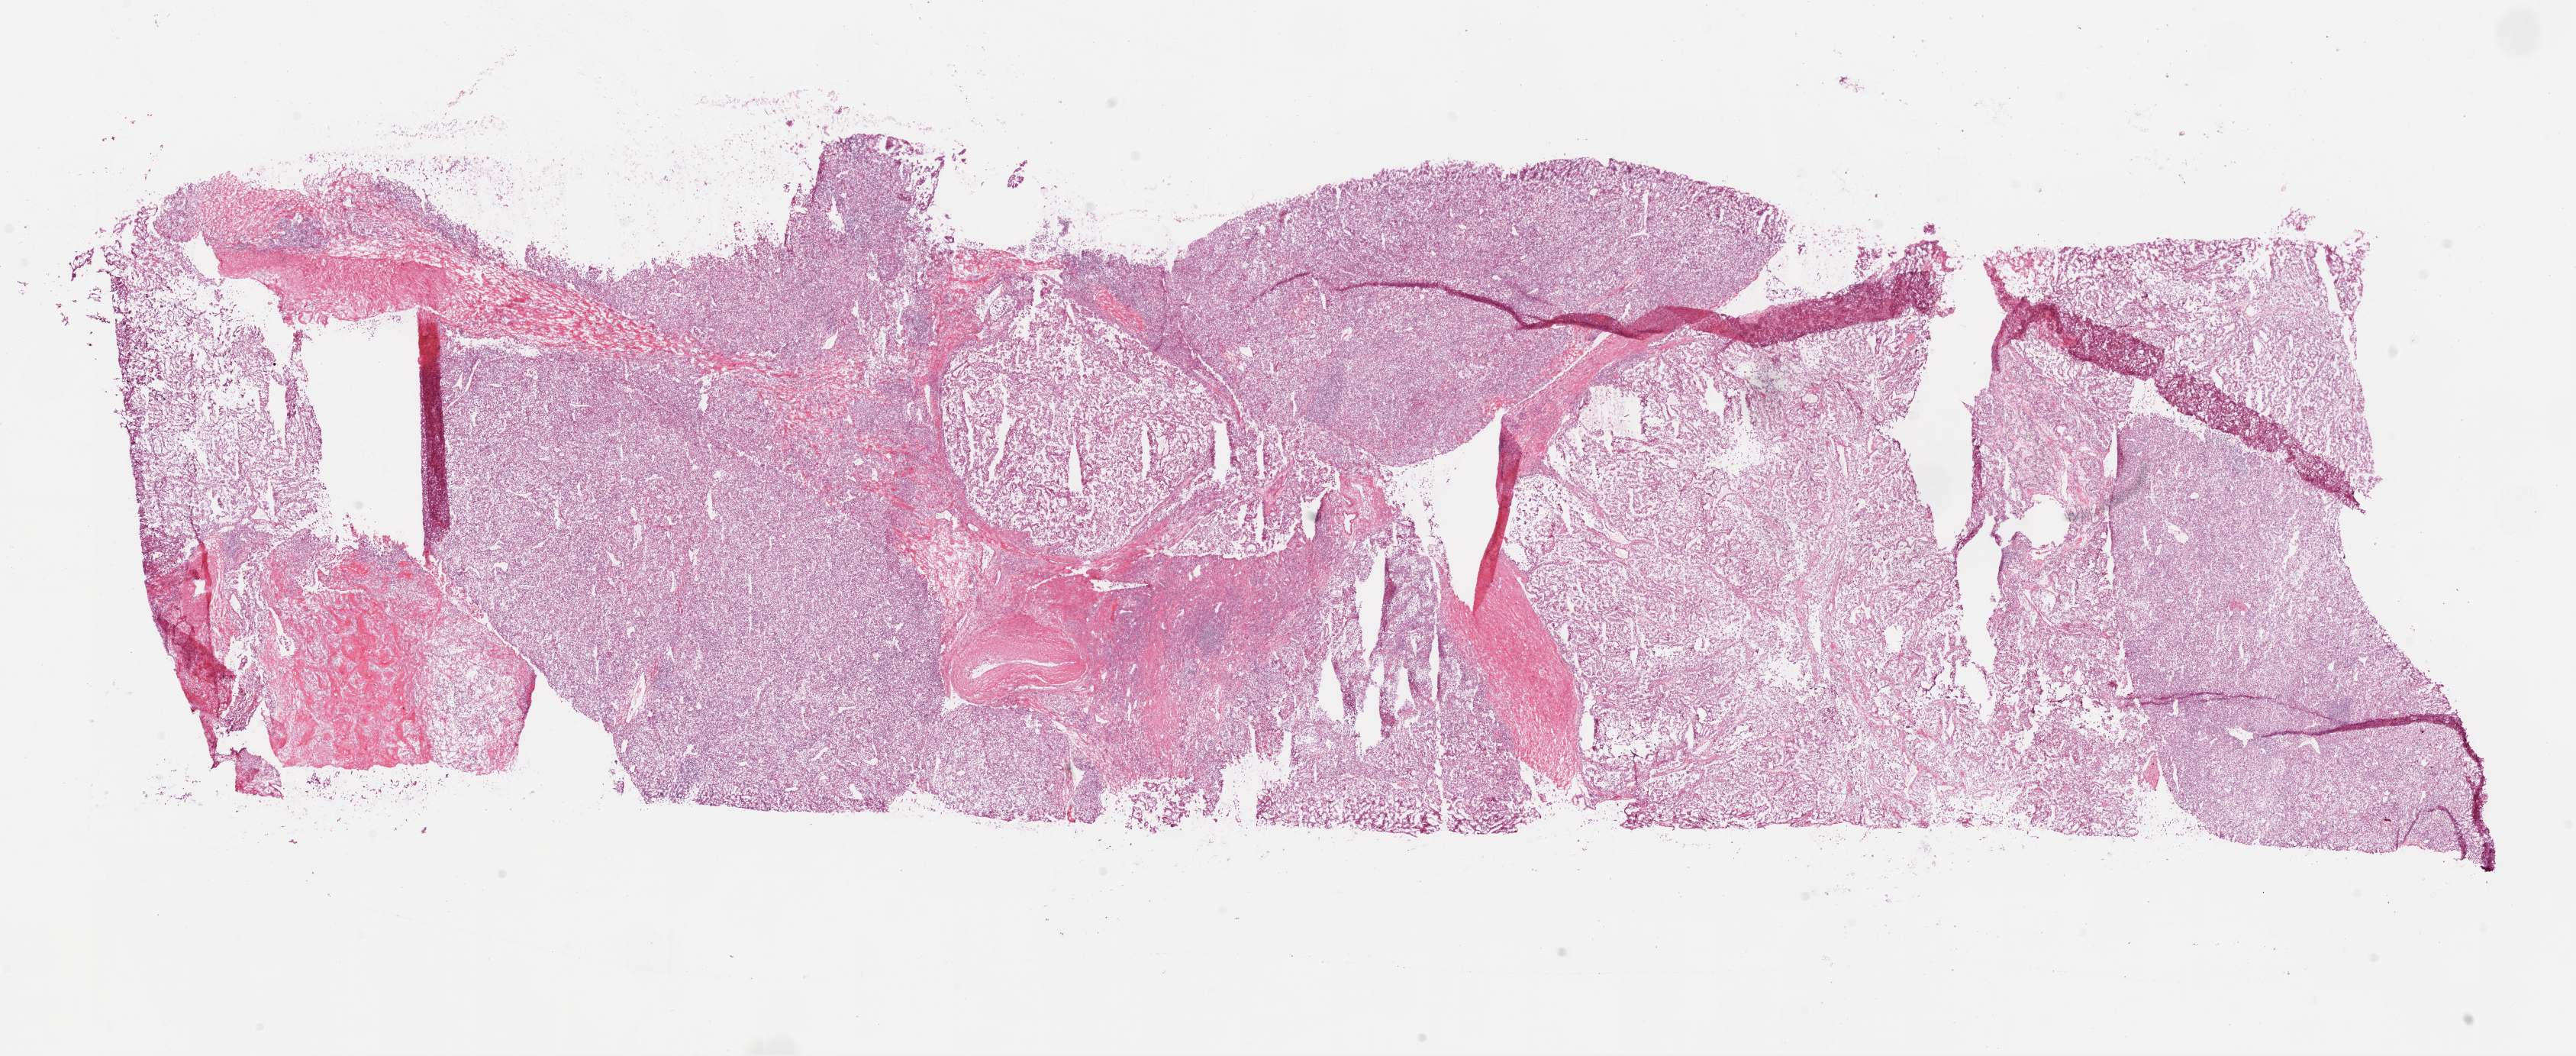
Digitized H&E tissue section (whole slide) — low-resolution overview of the scanned area, about 27.1 x 11.1 mm (slide scanned at 20x); frozen section; kidney, primary tumour sample. Female patient; age at initial diagnosis 55 years.
Pathologic diagnosis: Clear cell adenocarcinoma, NOS.